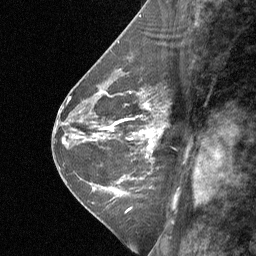
Breast MRI (dynamic contrast-enhanced), one sagittal slice; dynamic contrast-enhanced study with each time point stored as its own series, time point 2 of 3 at this slice position (early post-contrast, ordered by acquisition time); 1.5 T; TE 4.8 ms, TR 27 ms; 2 mm slice thickness; 256 × 256 image matrix, field of view 180 × 180 mm. Patient: female, 42 years. From the clinical record (not read from this slice): setting: breast cancer imaged before/during neoadjuvant chemotherapy; receptor status: triple-negative.
Outlined on this slice (semi-automatically segmented with operator editing):
- analysis volume of interest (the breast-tissue region the enhancement analysis was run in; not a lesion): bounding box <124,94,167,161> (left, top, right, bottom; pixels)
- tumour enhancement mask (voxels above the 90 % enhancement threshold inside the analysis volume of interest): <145,105,163,147>